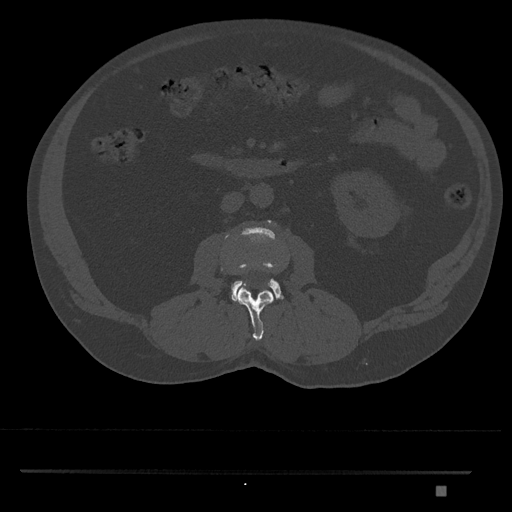
CT including the spine, one axial slice. Slice 721 of 1134 in the series (ordered by position). Reconstruction kernel Br40s/3. Bone window (W 1800 / L 400 HU). 512 × 512 image matrix. Male patient, age 65 years. Case-level facts recorded for this patient, not image findings: primary cancer: prostate.
Structures marked on this image (semi-automatic segmentation, software-assisted and operator-edited):
- L2 vertebra: box from (x=236, y=287) to (x=274, y=341) px
- L3 vertebra: (x=231, y=220)–(x=284, y=303)